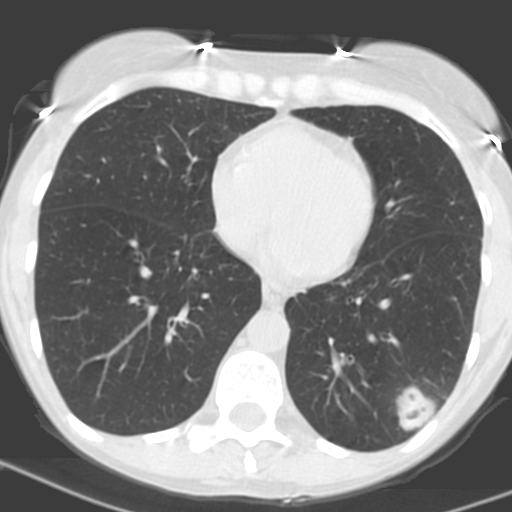
Low-dose screening chest CT, one axial slice; slice 60 of 156 in the series (ordered by position); lung window (W 1500 / L -600 HU); 512 × 512 image matrix.
Annotated regions visible in this slice (outlined manually by an expert reader):
- lesion 1 (tumor, lower lobe of left lung): bounding box (x1, y1, x2, y2) in pixels: (396, 386, 437, 431)